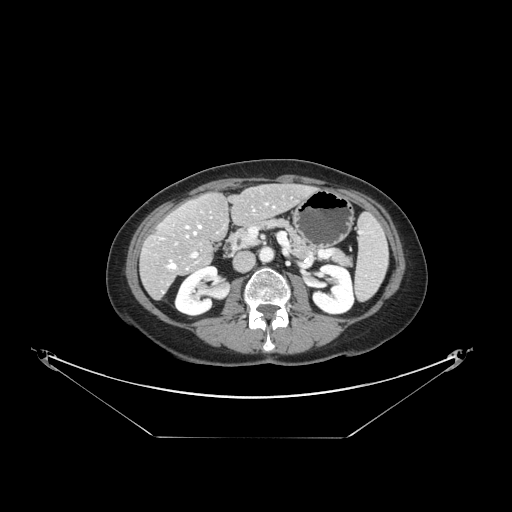
Contrast-enhanced abdominal CT, one axial slice; slice 64 of 148 in the series (ordered by position); 120 kVp; intravenous contrast given; soft-tissue window (W 400 / L 40 HU); 2.5 mm slice thickness; 512 × 512 image matrix, field of view 500 × 500 mm. Female patient, age 73 years. From the clinical record (not read from this slice): diagnosis: colorectal cancer liver metastases, imaged before liver resection; multiple liver metastases: no; largest metastasis: 1 cm; chemotherapy before resection: yes.
Structures marked on this image (expert manual segmentation):
- hepatic veins: bounding box <167,210,254,269> (left, top, right, bottom; pixels)
- liver: <142,185,312,298>
- planned liver remnant (the part of the liver to remain after resection): <166,185,311,250>
- portal vein (with intrahepatic branches): <192,253,197,257>